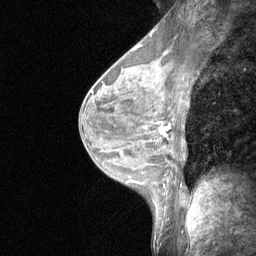
Breast MRI (dynamic contrast-enhanced), one sagittal slice. Slice 34 of 64 in the series (ordered by position). Dynamic contrast-enhanced study with each time point stored as its own series, time point 2 of 3 at this slice position (early post-contrast, ordered by acquisition time). 1.5 T. TE 4.8 ms, TR 27 ms. 2 mm slice thickness. 256 × 256 image matrix, field of view 200 × 200 mm. Female patient, age 44 years. From the clinical record (not read from this slice): setting: breast cancer imaged before/during neoadjuvant chemotherapy; receptor status: HR-positive, HER2-negative.
Outlined on this slice (semi-automatic segmentation, software-assisted and operator-edited):
- analysis volume of interest (the breast-tissue region the enhancement analysis was run in; not a lesion): bounding box (x1, y1, x2, y2) in pixels: (140, 109, 180, 148)
- tumour enhancement mask (voxels above the 90 % enhancement threshold inside the analysis volume of interest): (159, 128, 166, 135)